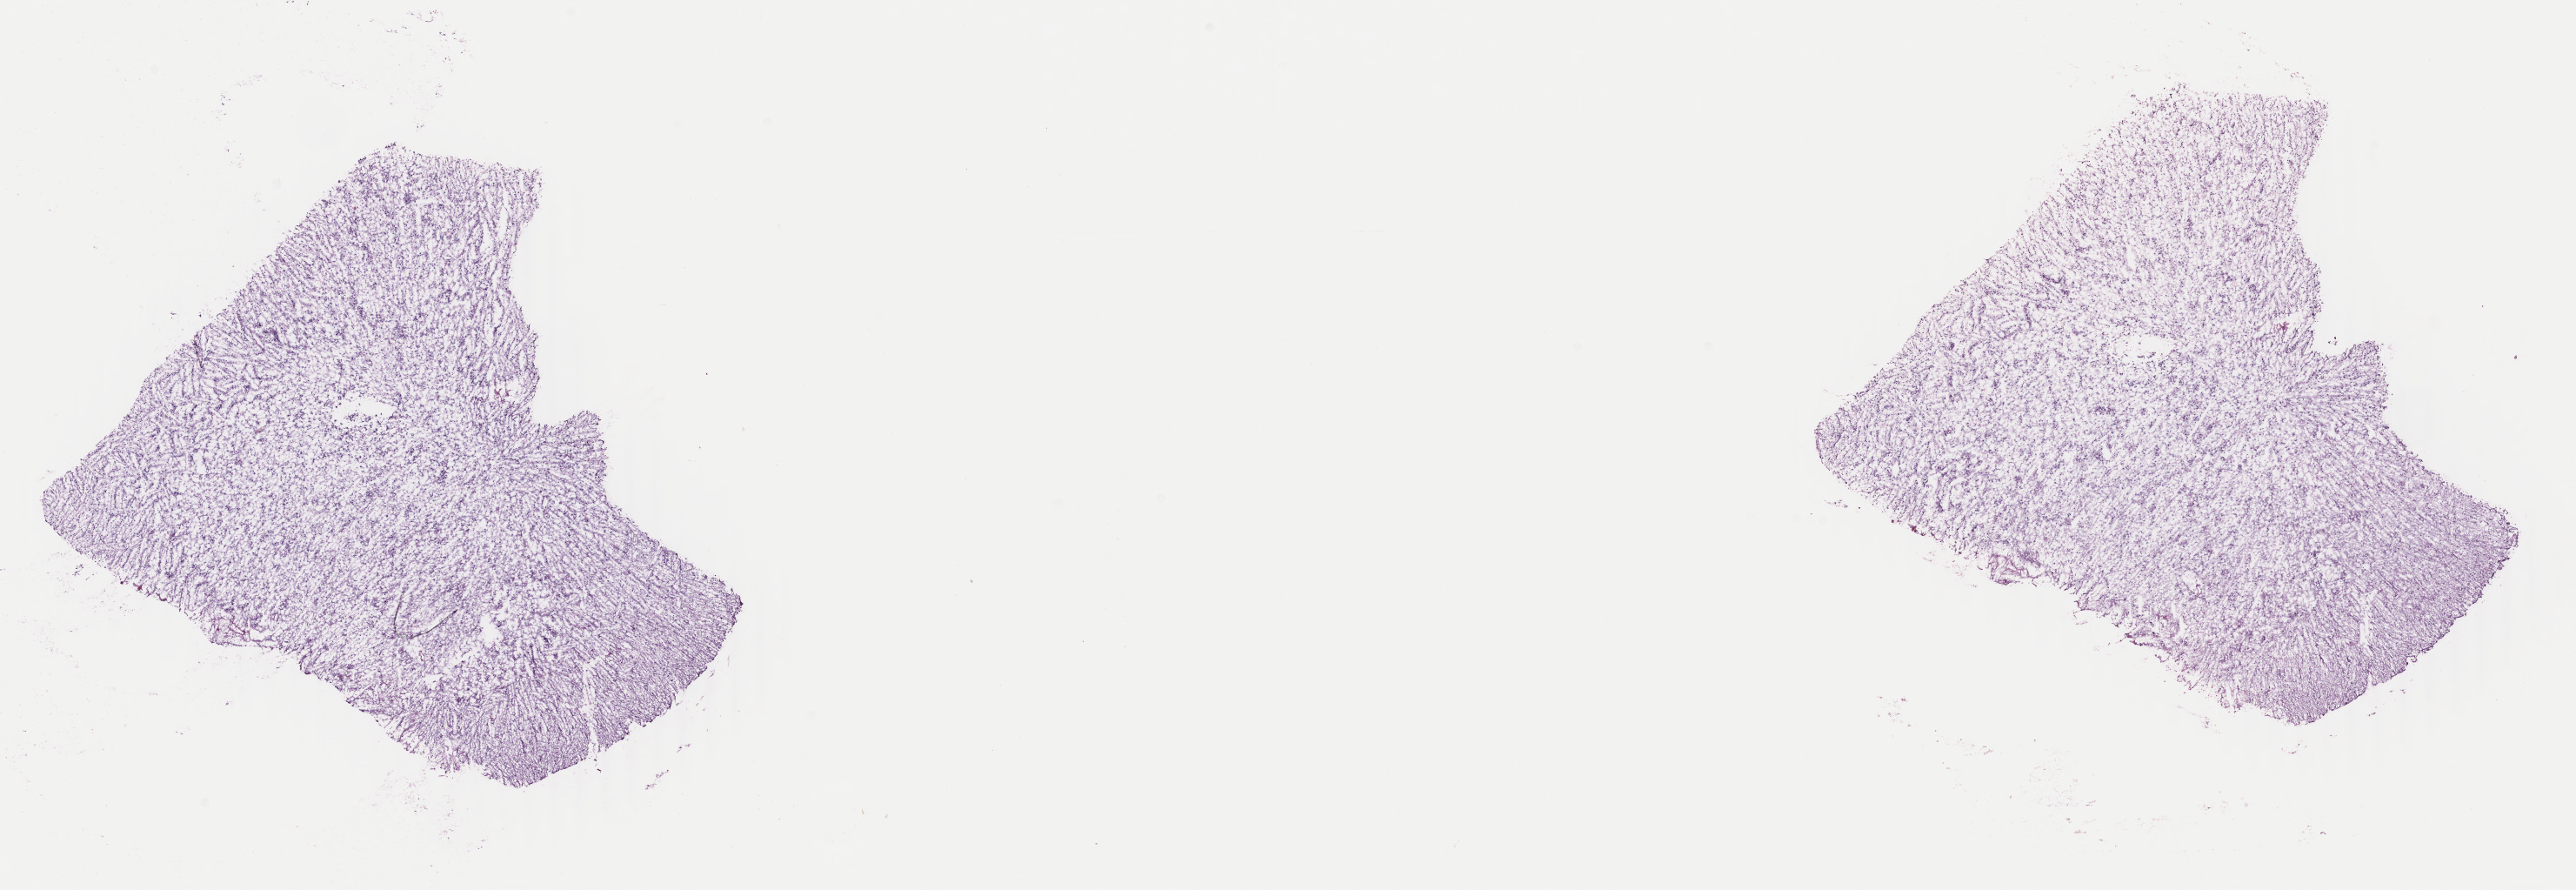
Whole-slide histology image, H&E-stained, low-resolution overview of the scanned area, about 23.6 x 8.1 mm, frozen section from the top of the tissue portion, sample: primary tumour, brain. Female, age 54 years at initial diagnosis. Histologic grade: G3 (poorly differentiated). Pathologist review of this section (percent, as recorded): tumour cells 40%, tumour nuclei 80%, normal cells 10%, stromal cells 50%, necrosis 0%. Infiltration values recorded for this section: lymphocyte infiltration 0%, monocyte infiltration 0%, neutrophil infiltration 0%.
Histologic diagnosis: Astrocytoma, anaplastic (cerebrum). Laterality: left.